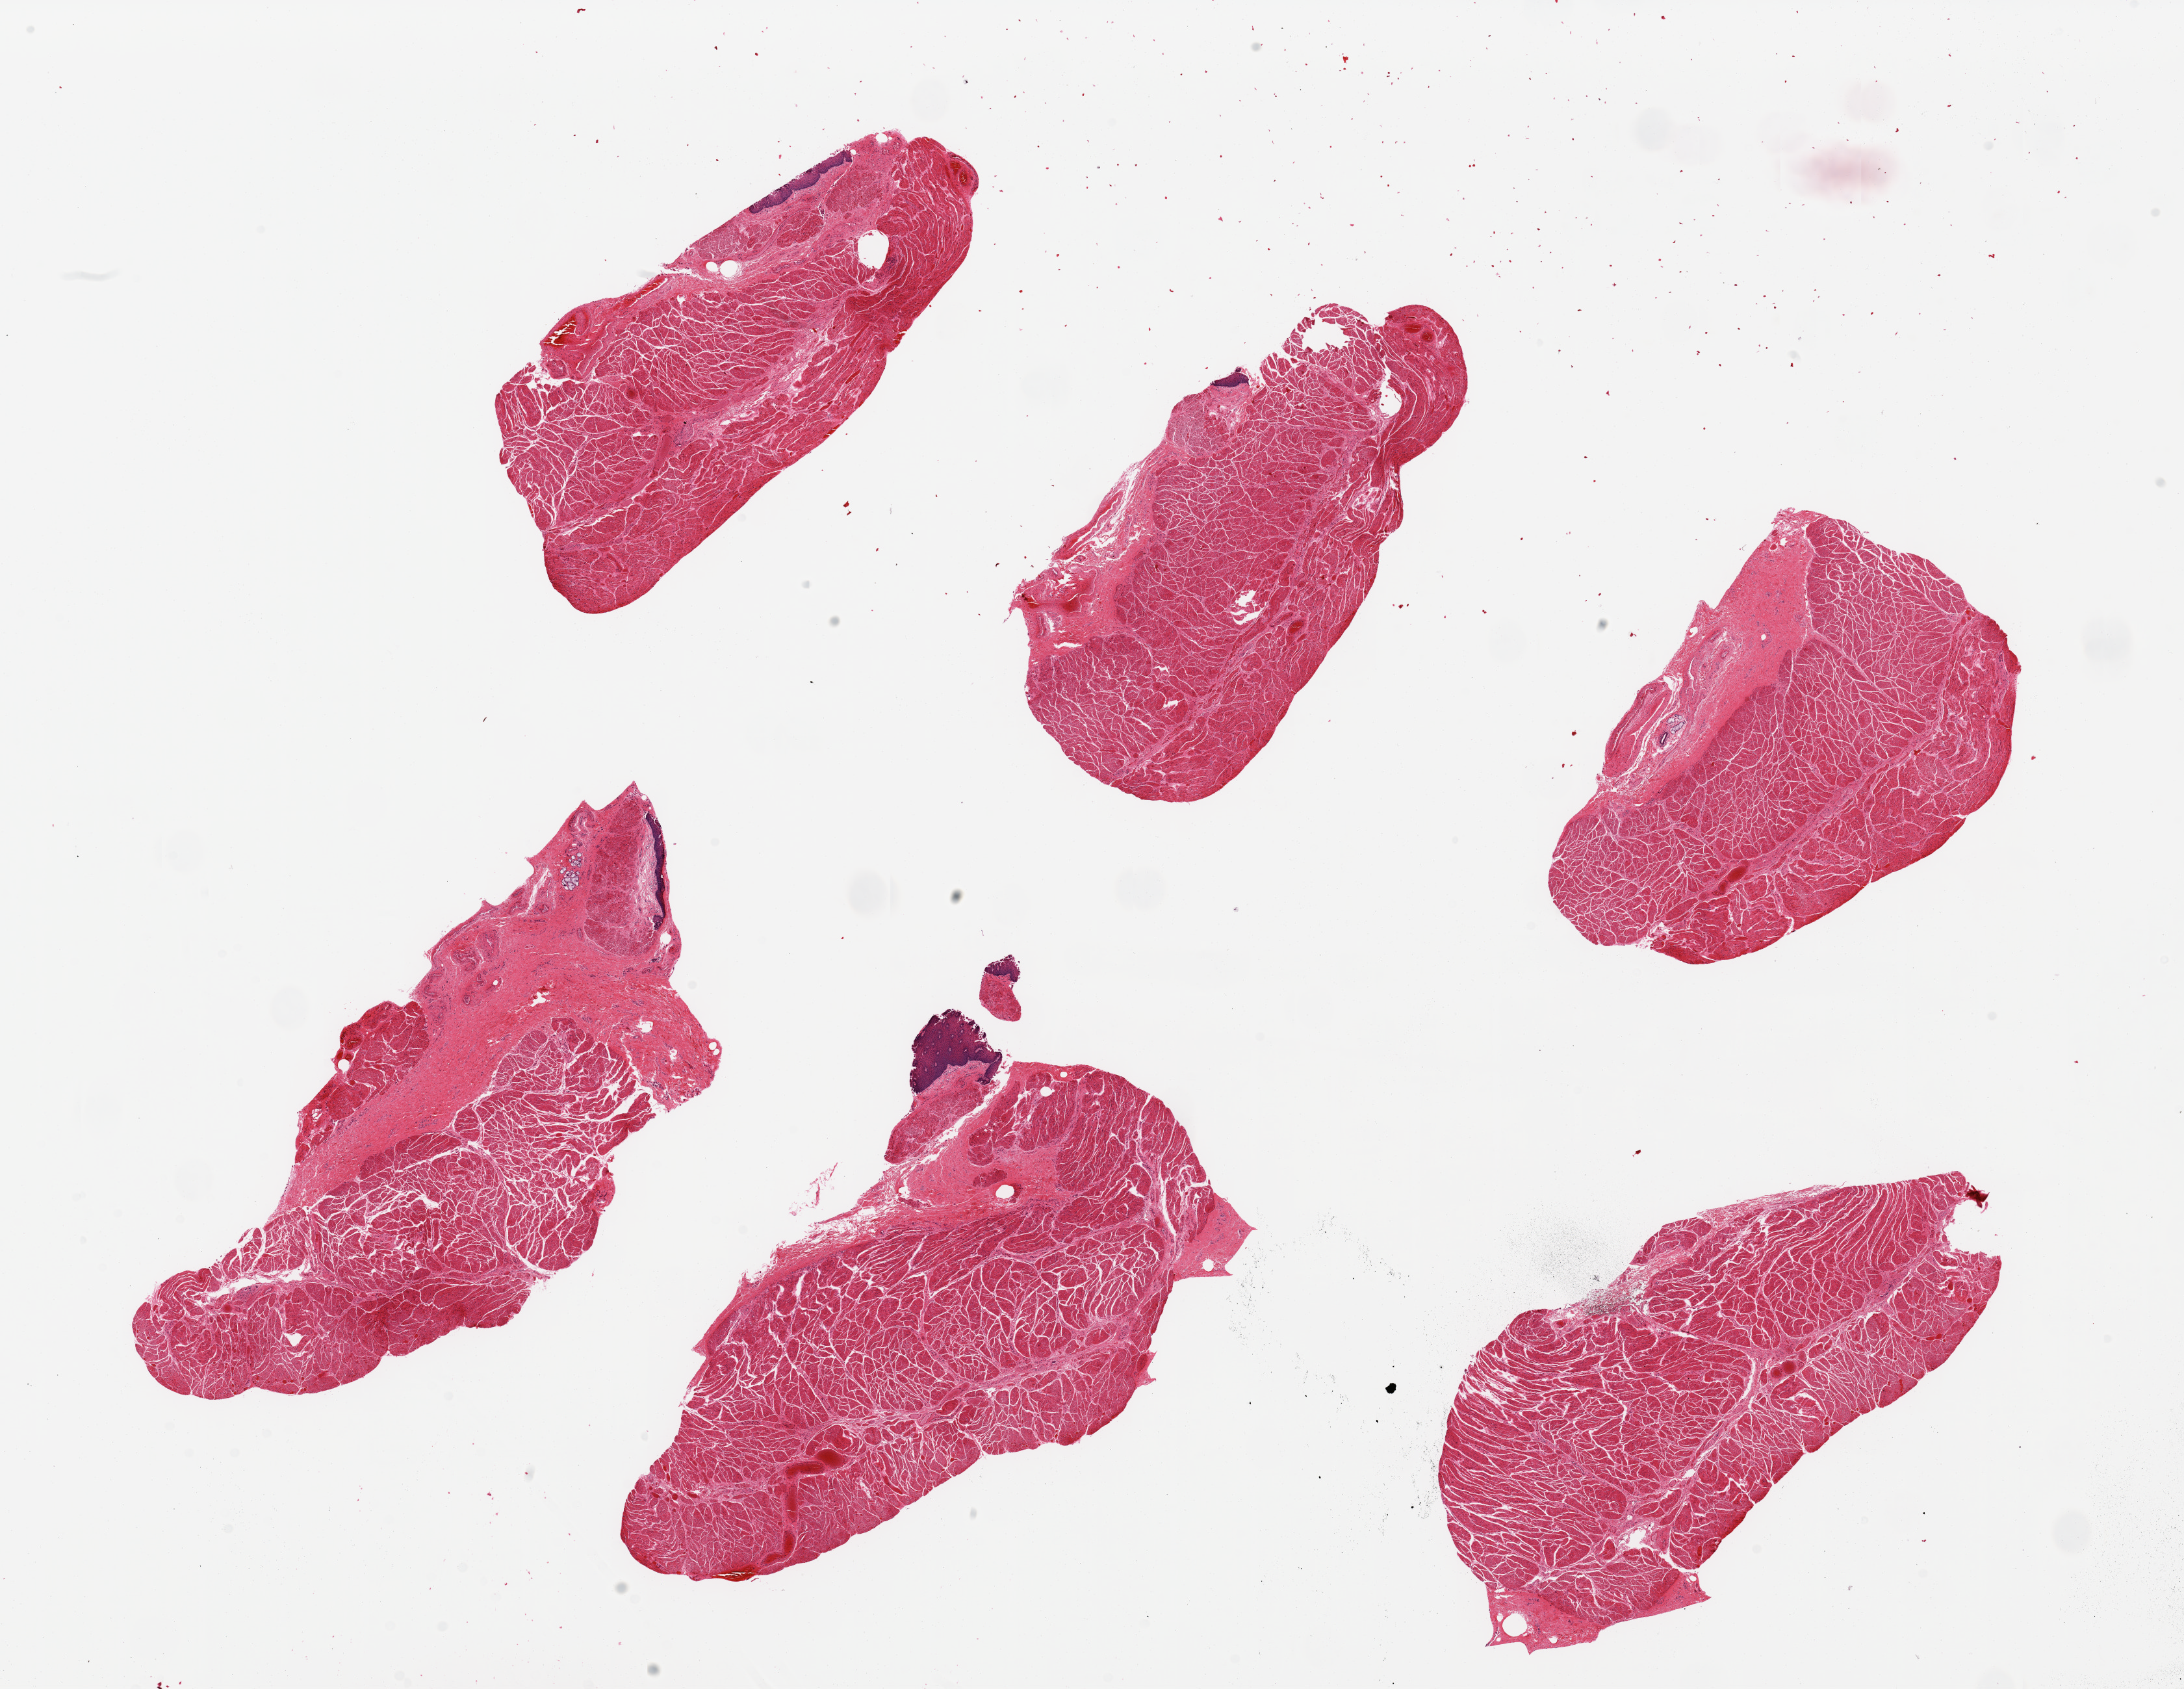
Haematoxylin and eosin whole-slide image, a low-resolution overview of the entire scanned area, about 26.6 x 20.6 mm; PAXgene-fixed paraffin-embedded (PFPE) section; target tissue: esophageal muscle; donor tissue sample.
Review note (as recorded): 6 pieces, predominantly muscularis, but with some residual mucosa.